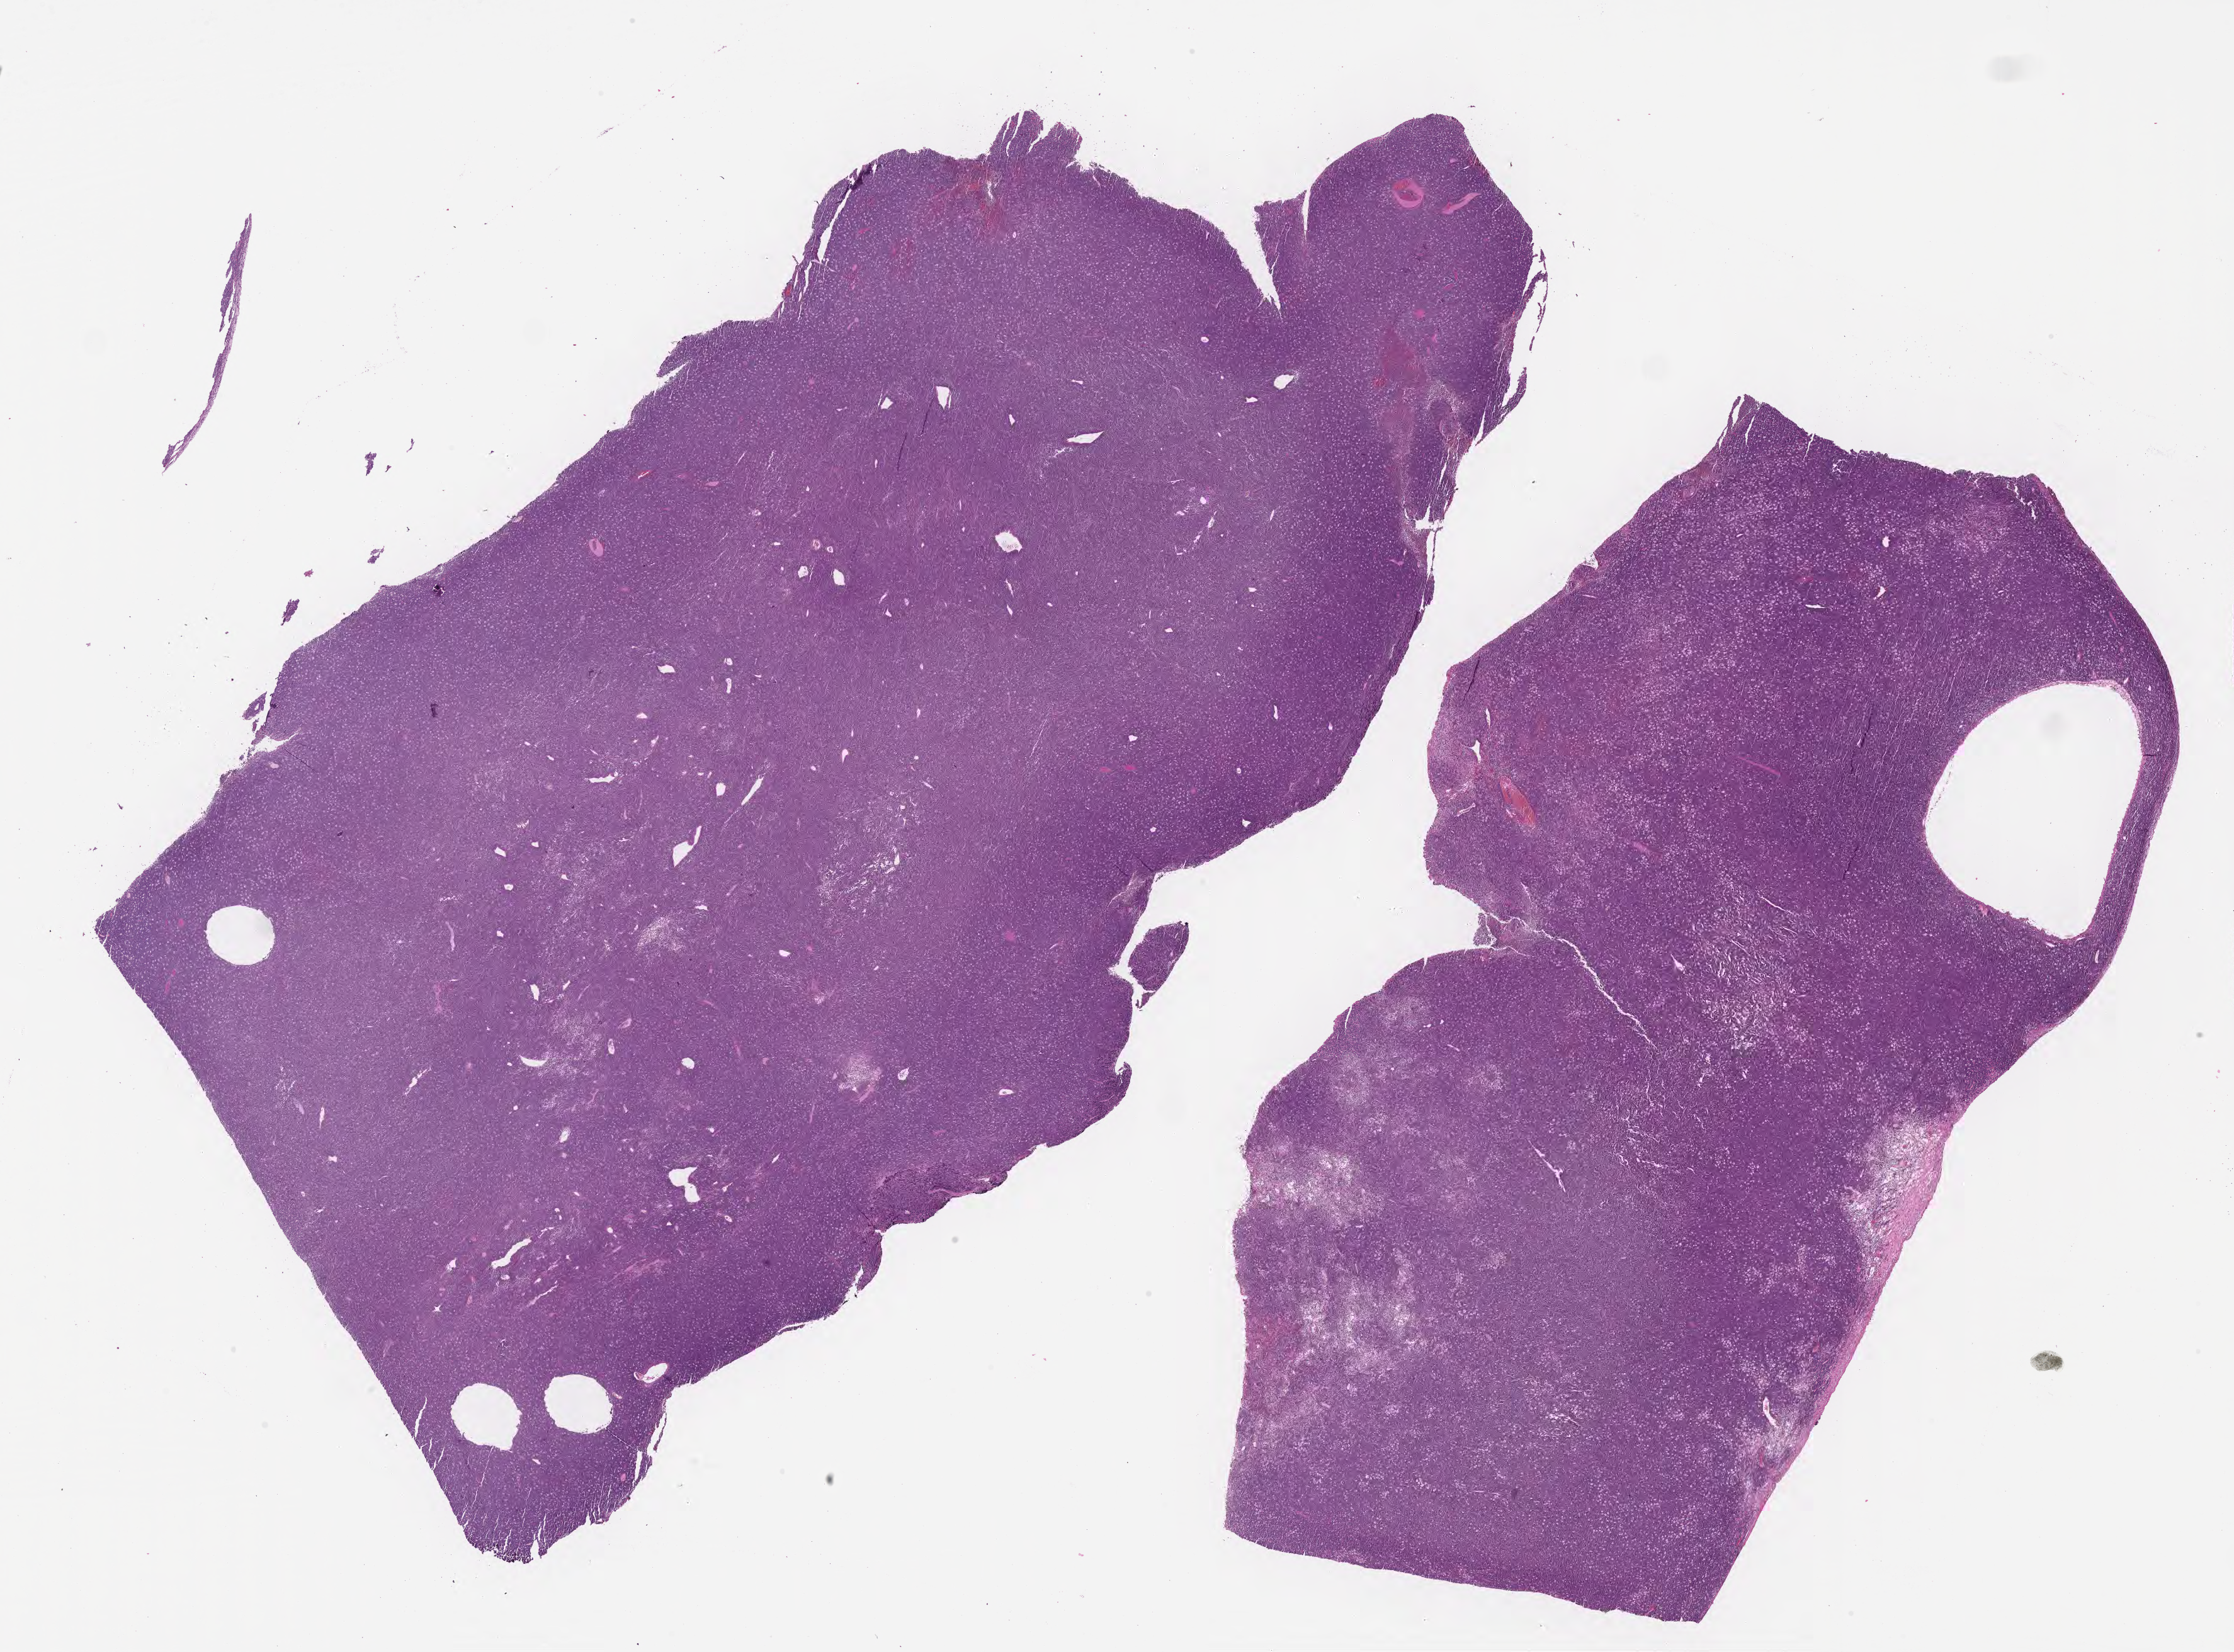
H&E whole-slide image — whole scanned area (about 28.7 x 21.2 mm) shown as a low-resolution overview. Formalin-fixed paraffin-embedded section. Specimen: primary tumor. Female patient, age 34 years. Composition of this section per pathologist review: tumor cells 90%, tumor nuclei 95%, stromal cells 5%, necrosis 5%, normal cells 0%. Infiltration values recorded for this section: lymphocyte infiltration 30%, monocyte infiltration 30%, neutrophil infiltration 5%.
Section: bottom of the tissue portion. Ann Arbor stage (patient): Stage IV. Diagnosis: Burkitt lymphoma, NOS.